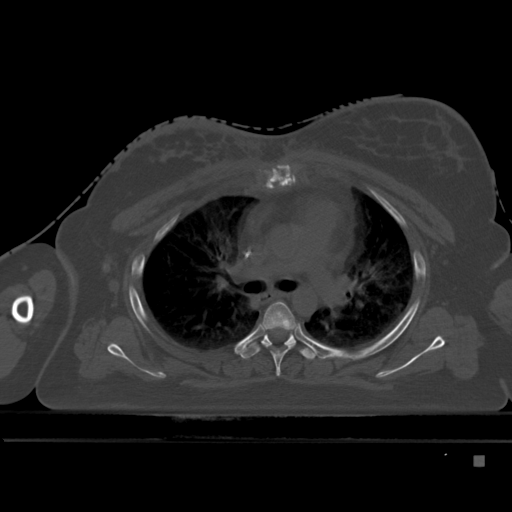
CT including the spine, one axial slice. Position 326 of 495 along the scan axis. Bone window (W 1800 / L 400 HU). 1.5 mm slice thickness. 512 × 512 image matrix, field of view 404 × 404 mm. Patient: female, 33 years. From the clinical record (not read from this slice): primary cancer: breast; vertebrae with lytic lesions (as recorded): T1.
Outlined on this slice (semi-automatically segmented with operator editing):
- T4 vertebra: box from (x=261, y=300) to (x=297, y=377) px
- T5 vertebra: (x=241, y=330)–(x=316, y=360)